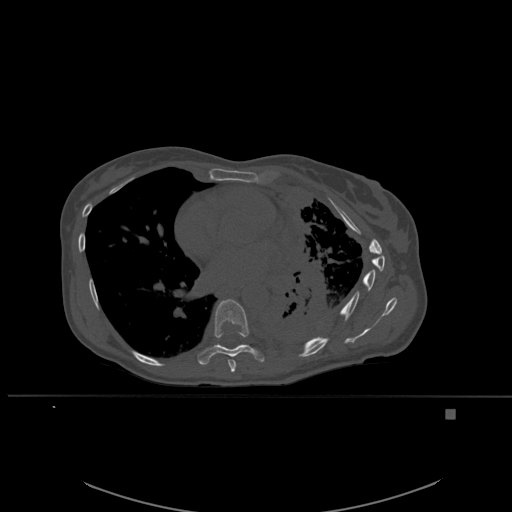
CT including the spine, one axial slice; position 351 of 537 along the scan axis; bone window (W 1800 / L 400 HU); 1.5 mm slice thickness; 512 × 512 image matrix. Female patient, age 45 years. From the clinical record (not read from this slice): primary cancer: lung.
Annotated regions visible in this slice (semi-automatic segmentation, software-assisted and operator-edited):
- T7 vertebra: box from (x=228, y=360) to (x=236, y=373) px
- T8 vertebra: (x=196, y=299)–(x=265, y=365)